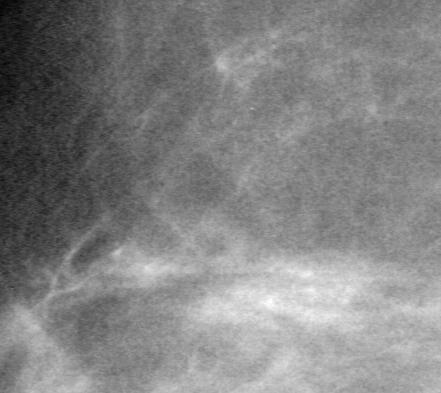
Cropped region of a digitized screen-film mammogram centred on a radiologist-marked abnormality, left breast, MLO view, BI-RADS breast density category 2 (scale 1–4).
- Finding: calcifications, morphology pleomorphic, distribution clustered; BI-RADS assessment category 4; pathology result (as recorded, not read from the image): malignant.